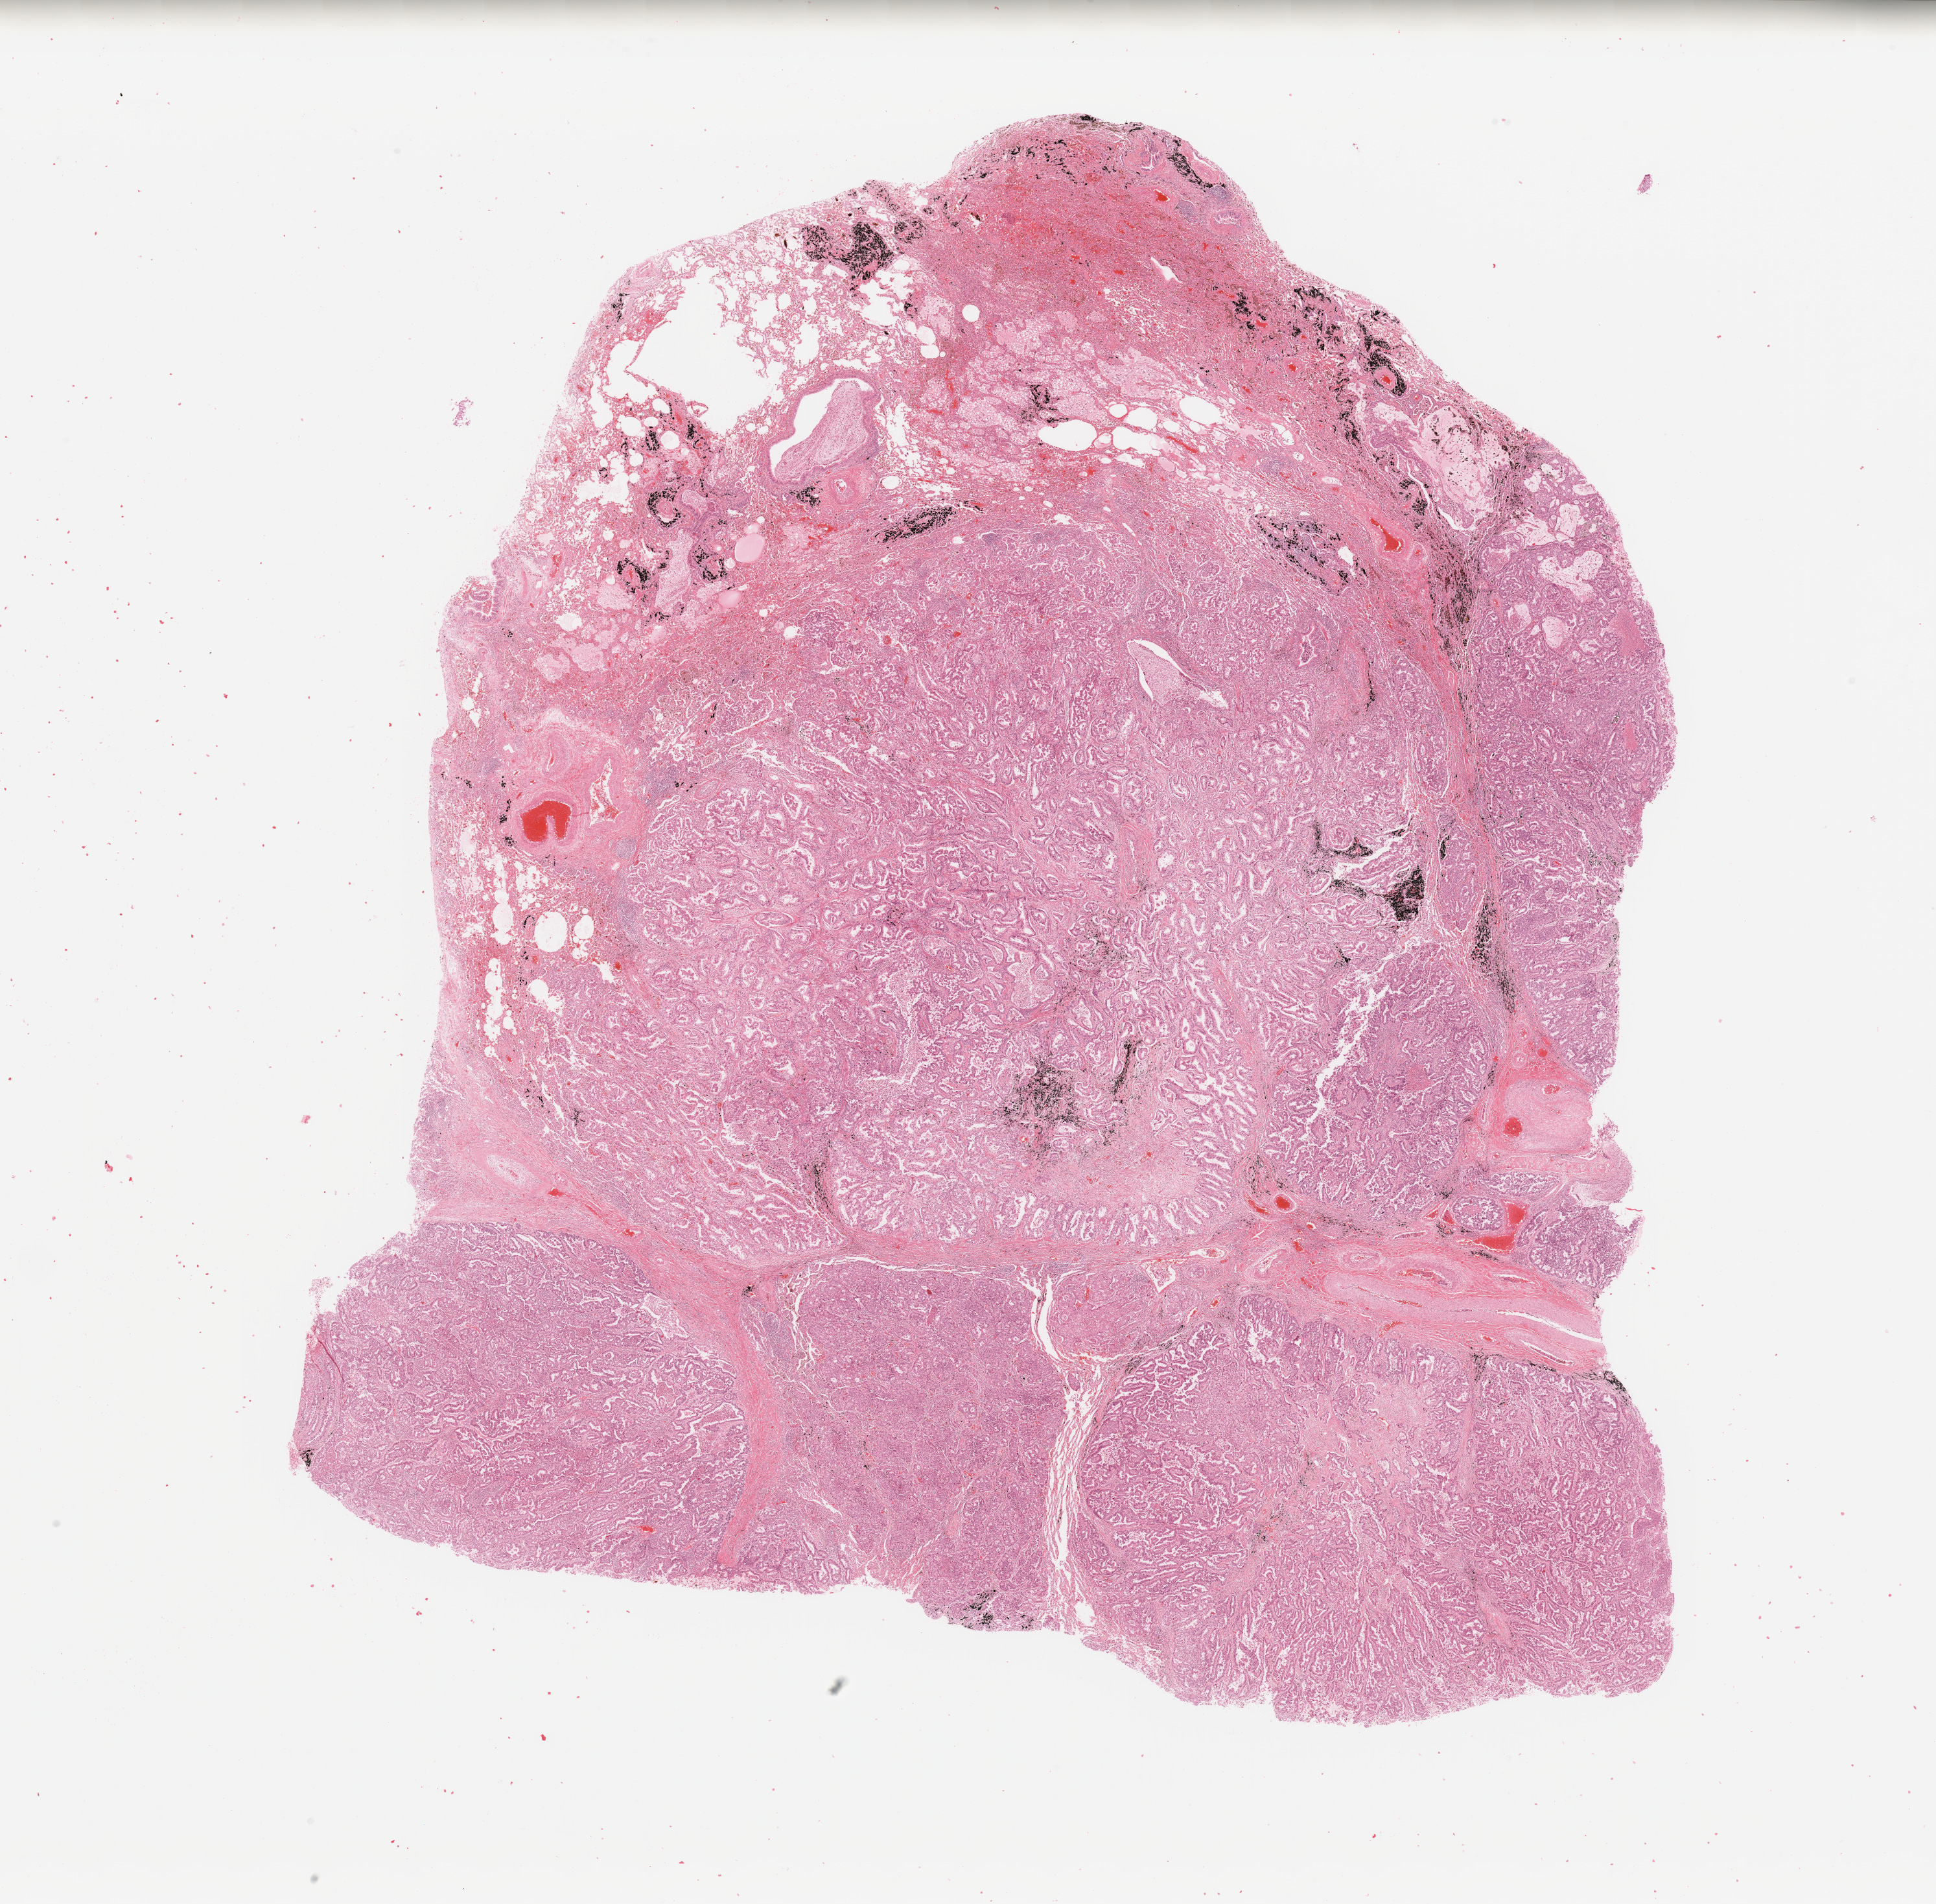
Digitized Hematoxylin and eosin (H&E) stained tissue section (whole slide), whole scanned area (about 23.6 x 23.2 mm, slide scanned at 20x) shown as a low-resolution overview; tumour tissue sample, sampled site: lung. 56-year-old male patient. Histologic grade: G3 (poorly differentiated). Pathologist review of this section (percent, as recorded): tumour nuclei 70%, necrosis 5%.
AJCC pathologic stage: IIIA. Histologic diagnosis: Adenocarcinoma, NOS.